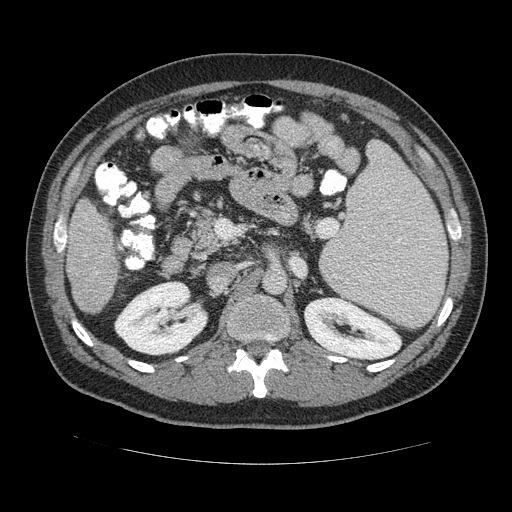
Contrast-enhanced abdominal CT (liver protocol), one axial slice; slice 58 of 113 in the series (ordered by position); 120 kVp; soft-tissue window (W 400 / L 40 HU); 512 × 512 image matrix, field of view 400 × 400 mm. From the clinical record (not read from this slice): diagnosis: hepatocellular carcinoma (patient treated with transarterial chemoembolisation; whether this scan precedes or follows treatment is not stated here); TNM stage (as recorded): Stage-II; Child-Pugh class: B; tumour differentiation: moderately differentiated; tumour nodularity: multinodular.
Annotated regions visible in this slice (semi-automatic segmentation, software-assisted and operator-edited):
- liver parenchyma outside the tumour (the mass and vessels are separate outlines, so this box may not span the whole liver): bounding box <64,196,120,314> (left, top, right, bottom; pixels)
- liver vessels: <85,220,95,274>